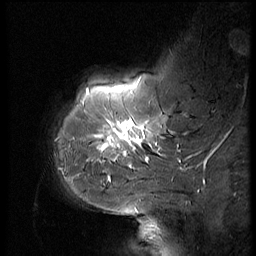
Breast MRI (dynamic contrast-enhanced), one sagittal slice; position 13 of 56 along the scan axis; dynamic contrast-enhanced series, image 2 of 3 at this slice position (ordered by acquisition); 1.5 T; TE 4.2 ms, TR 9 ms; 2.5 mm slice thickness; 256 × 256 image matrix, field of view 180 × 180 mm. Female patient, age 61 years. Case-level facts recorded for this patient, not image findings: setting: breast cancer imaged before/during neoadjuvant chemotherapy; receptor status: HR-positive, HER2-negative.
Outlined on this slice (semi-automatic segmentation, software-assisted and operator-edited):
- analysis volume of interest (the breast-tissue region the enhancement analysis was run in; not a lesion): bounding box <65,74,185,175> (left, top, right, bottom; pixels)
- tumour enhancement mask (voxels above the 140 % enhancement threshold inside the analysis volume of interest): <97,119,148,169>